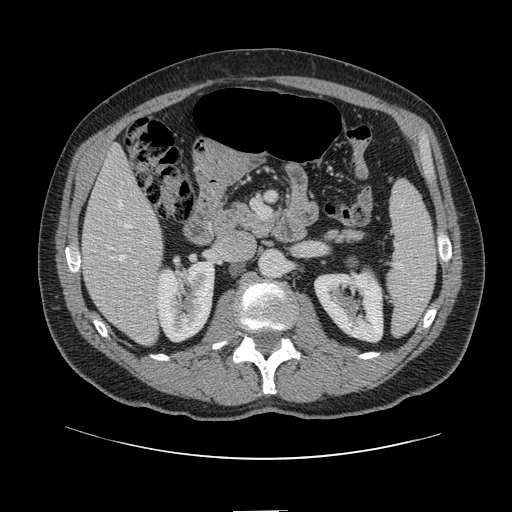
Contrast-enhanced abdominal CT, one axial slice; slice 47 of 161 in the series (ordered by position); 120 kVp; intravenous contrast given; soft-tissue window (W 400 / L 40 HU); 2.5 mm slice thickness; 512 × 512 image matrix, field of view 412 × 412 mm. Male patient, age 66 years. Case-level facts recorded for this patient, not image findings: diagnosis: colorectal cancer liver metastases, imaged before liver resection; multiple liver metastases: no; largest metastasis: 3.5 cm; disease in both lobes: no.
Annotated regions visible in this slice (outlined manually by an expert reader):
- hepatic veins: box from (x=120, y=200) to (x=130, y=261) px
- liver: (x=82, y=150)–(x=162, y=345)
- planned liver remnant (the part of the liver to remain after resection): (x=82, y=150)–(x=158, y=274)